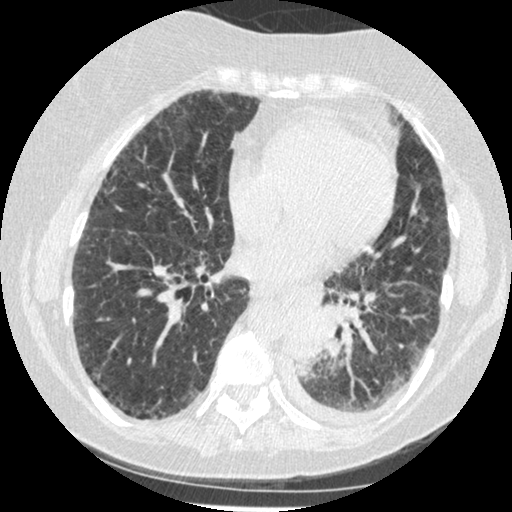
Low-dose screening chest CT, axial slice; third annual screen; lung window (W 1500 / L -600 HU); 1.25 mm slice thickness; slice 253 of 341 in the series; 512 × 512 image matrix. Female participant, aged 60 years at enrolment. Former smoker at enrolment.
- Expert-annotated lung lesion, bounding box <278,302,344,376> (left, top, right, bottom; pixels).
- Reader record for this screening exam (exam-level; its link to the box is not recorded): non-calcified nodule or mass ≥4 mm, left lower lobe, 54 × 38 mm, smooth margins, soft tissue attenuation, pre-existing on the prior screen: yes; interval growth: yes.
- Lung cancer was diagnosed 15 days after this screen: small cell carcinoma, NOS, left lower lobe, undifferentiated (G4), stage IV (AJCC 6th edition), 69 mm at pathology.